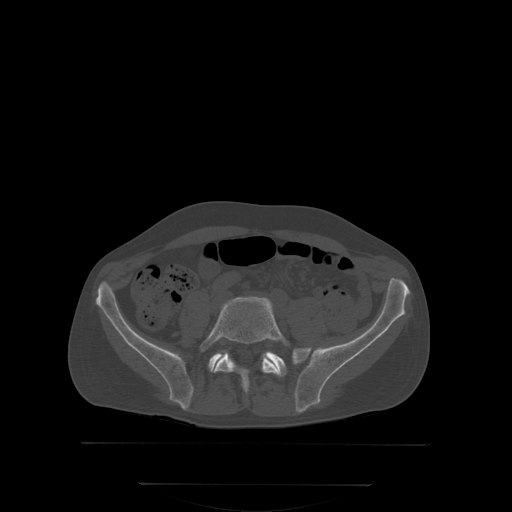
CT including the spine, one axial slice. Position 93 of 350 along the scan axis. Bone window (W 1800 / L 400 HU). 2.5 mm slice thickness. 512 × 512 image matrix, field of view 500 × 500 mm. Patient: male, 58 years. Case-level facts recorded for this patient, not image findings: primary cancer: prostate; vertebrae with lytic lesions (as recorded): L1.
Outlined on this slice (semi-automatic segmentation, software-assisted and operator-edited):
- L5 vertebra: bounding box <202,298,288,391> (left, top, right, bottom; pixels)